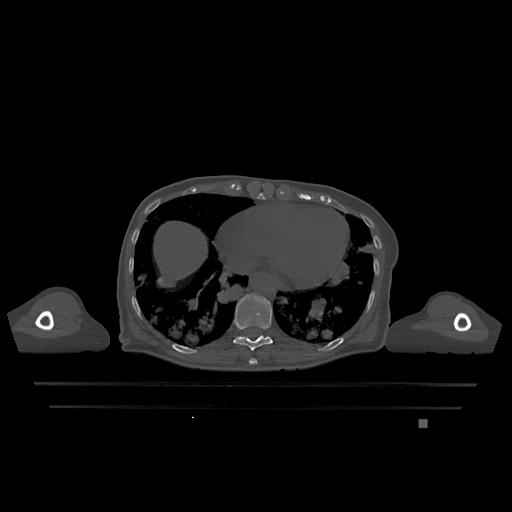
CT including the spine, one axial slice. Position 638 of 1317 along the scan axis. Bone window (W 1800 / L 400 HU). 512 × 512 image matrix, field of view 500 × 500 mm. Female patient, age 74 years. Case-level facts recorded for this patient, not image findings: primary cancer: lung.
Outlined on this slice (semi-automatically segmented with operator editing):
- T10 vertebra: bounding box <233,293,273,351> (left, top, right, bottom; pixels)
- T9 vertebra: <249,358,257,364>